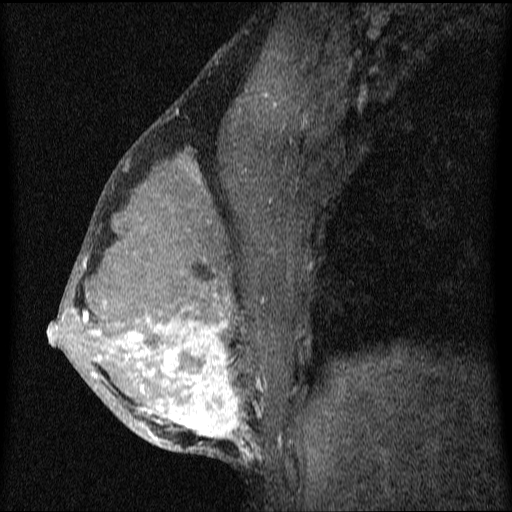
Breast MRI (dynamic contrast-enhanced), one sagittal slice. Dynamic contrast-enhanced series, image 2 of 4 at this slice position (ordered by acquisition). 1.5 T. TE 4.2 ms, TR 9.1 ms. 512 × 512 image matrix. Patient: female, 33 years.
Structures marked on this image (semi-automatic segmentation, software-assisted and operator-edited):
- analysis volume of interest (the breast-tissue region the enhancement analysis was run in; not a lesion): bounding box [x1, y1, x2, y2] px = [49, 151, 336, 458]
- tumour enhancement mask (voxels above the 70 % enhancement threshold inside the analysis volume of interest): [49, 180, 258, 458]